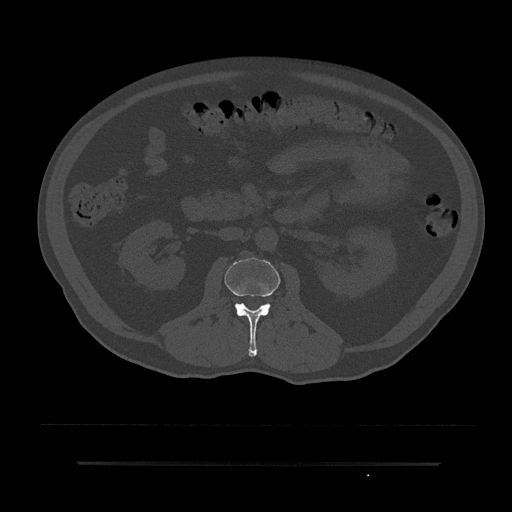
CT including the spine, one axial slice; position 65 of 797 along the scan axis; reconstruction kernel Br40s/3; 120 kVp; bone window (W 1800 / L 400 HU); 0.5 mm slice thickness; 512 × 512 image matrix, field of view 464 × 464 mm. Male patient, age 59 years. Case-level facts recorded for this patient, not image findings: primary cancer: bile ducts; vertebrae with lytic lesions (as recorded): T10.
Annotated regions visible in this slice (semi-automatically segmented with operator editing):
- L2 vertebra: bounding box [x1, y1, x2, y2] px = [225, 257, 280, 357]